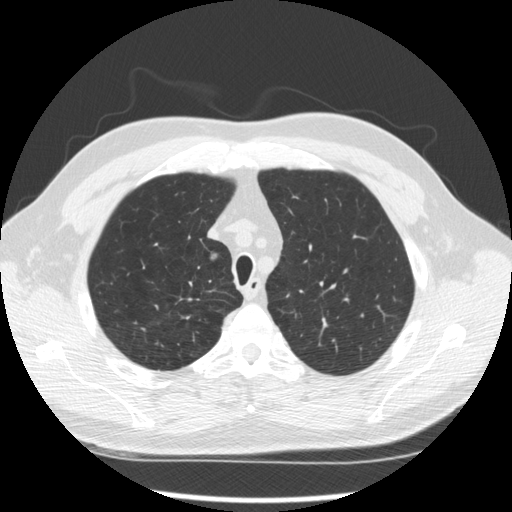
Axial slice from a low-dose chest CT screening exam, second screening round (one year after baseline), lung window (W 1500 / L -600 HU), slice 56 of 289 in the series, 512 × 512 image matrix. Male, age 64 years at enrolment.
Expert reader's lesion annotation, bounding box <195,244,226,275> (left, top, right, bottom; pixels). The screening reader recorded 3 non-calcified nodules or masses ≥4 mm on this exam; which of them this box marks is not recorded. Later outcome: lung cancer diagnosed 411 days after this screen — adenocarcinoma, NOS, right upper lobe, moderately differentiated (G2), stage IA (AJCC 6th edition), 14 mm at pathology.